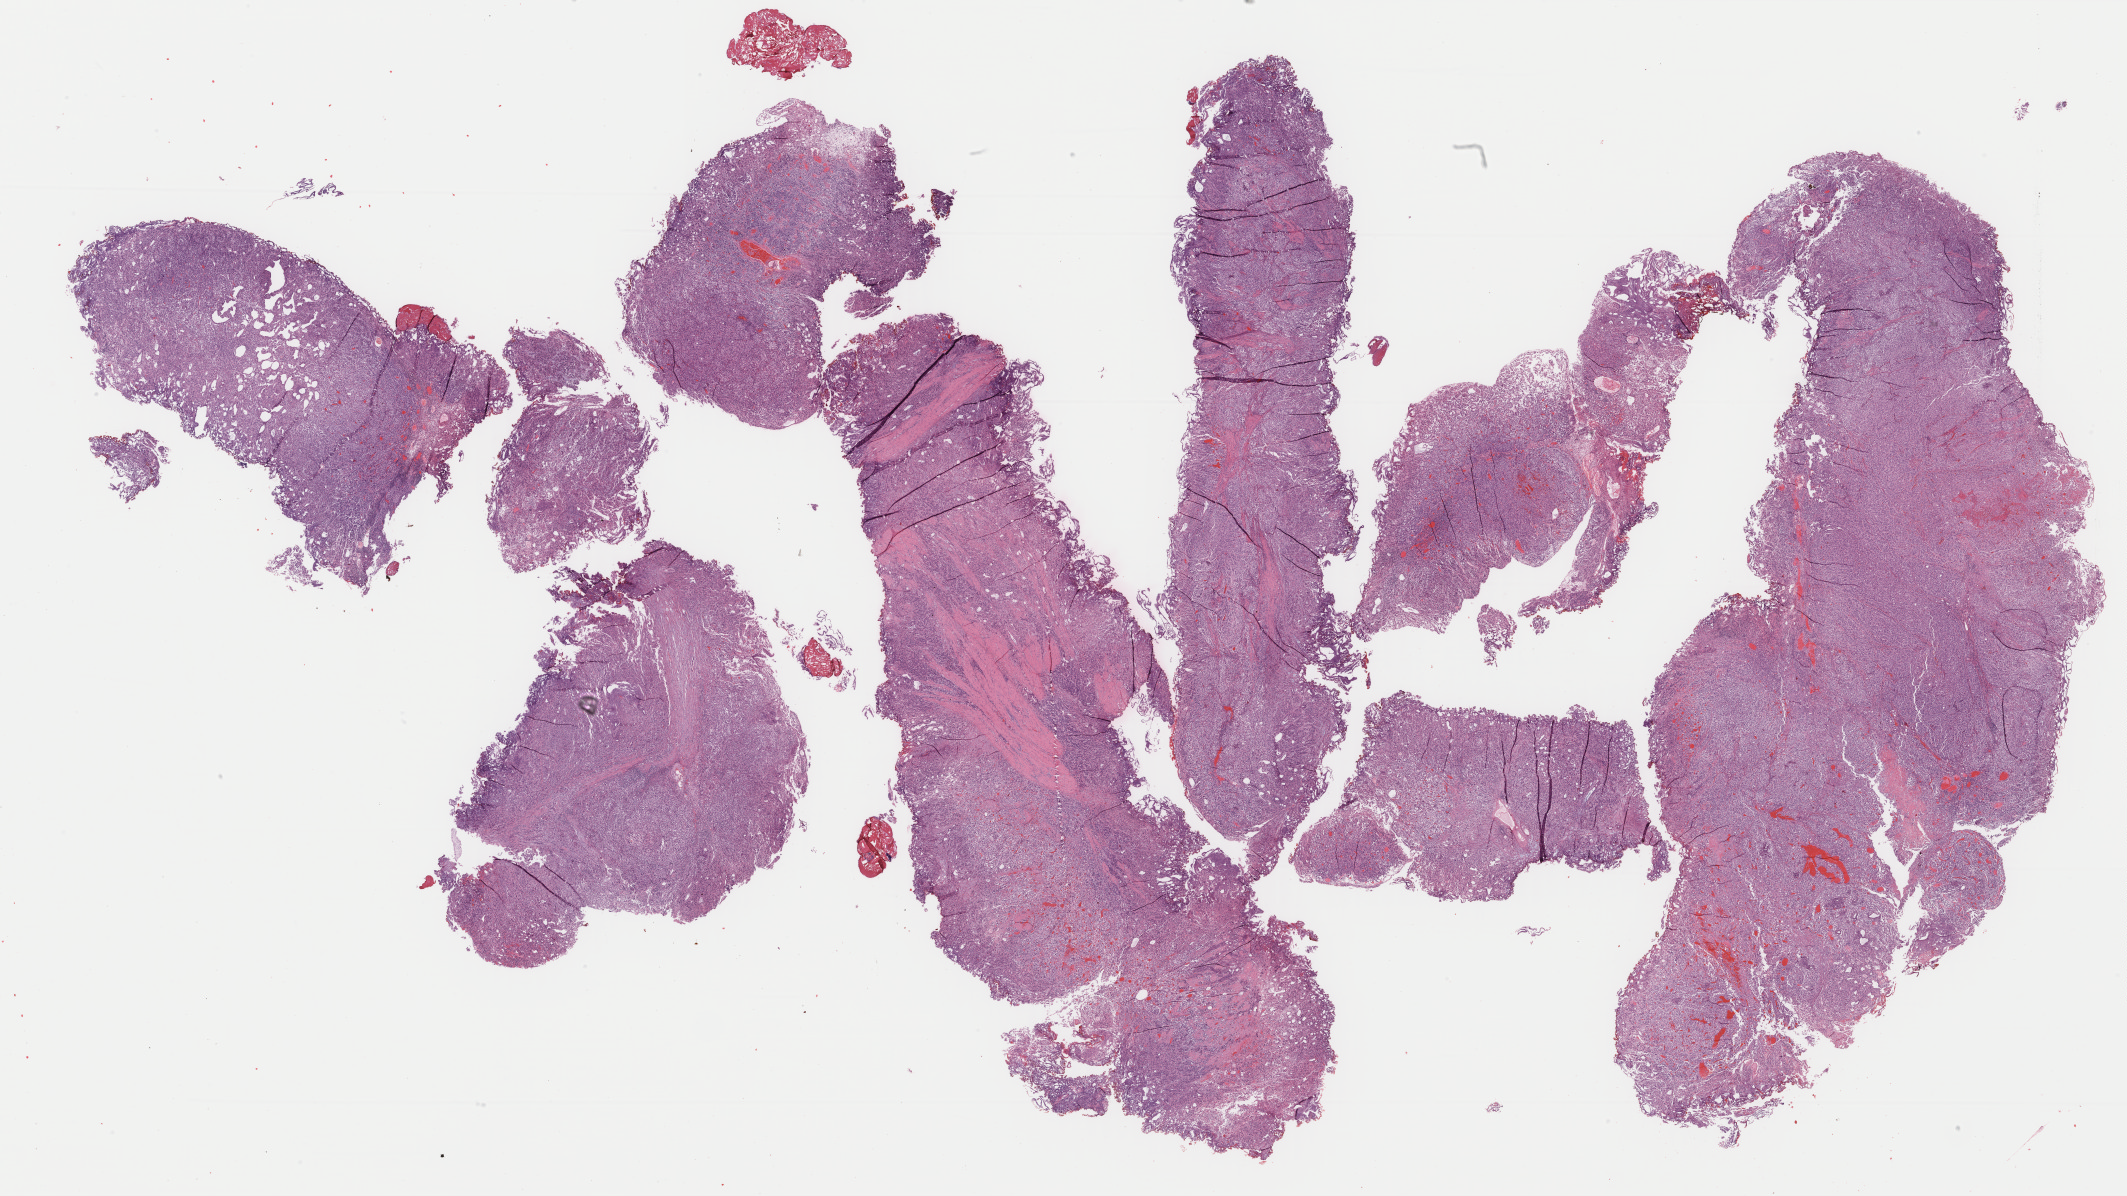
Digitized H&E-stained tissue section (whole slide) — a low-resolution overview of the entire scanned area, about 33.8 x 19.0 mm (acquisition: 40x scan), formalin-fixed paraffin-embedded (FFPE) diagnostic section, sample: primary tumour, bladder. Patient: male, age at initial diagnosis 51 years. Histologic grade: high grade.
• pathologic diagnosis: Transitional cell carcinoma
• AJCC pathologic stage: II (6th edition)